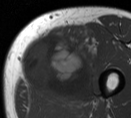
MRI of an extremity soft-tissue mass, one axial slice; slice 24 of 55 in the series (ordered by position); MR volume resampled by the dataset authors to the PET/CT grid (not the native acquisition matrix); 3.27 mm slice thickness; 131 × 118 image matrix, field of view 128 × 115 mm. Male patient. From the clinical record (not read from this slice): histological type: pleiomorphic liposarcoma; grade: high; site of the primary tumour: left thigh.
Structures marked on this image (expert contour drawn on MRI and transferred to this co-registered scan by the dataset authors):
- gross tumour volume including surrounding oedema: bounding box <20,23,103,102> (left, top, right, bottom; pixels)
- gross tumour volume (mass): <20,30,94,101>